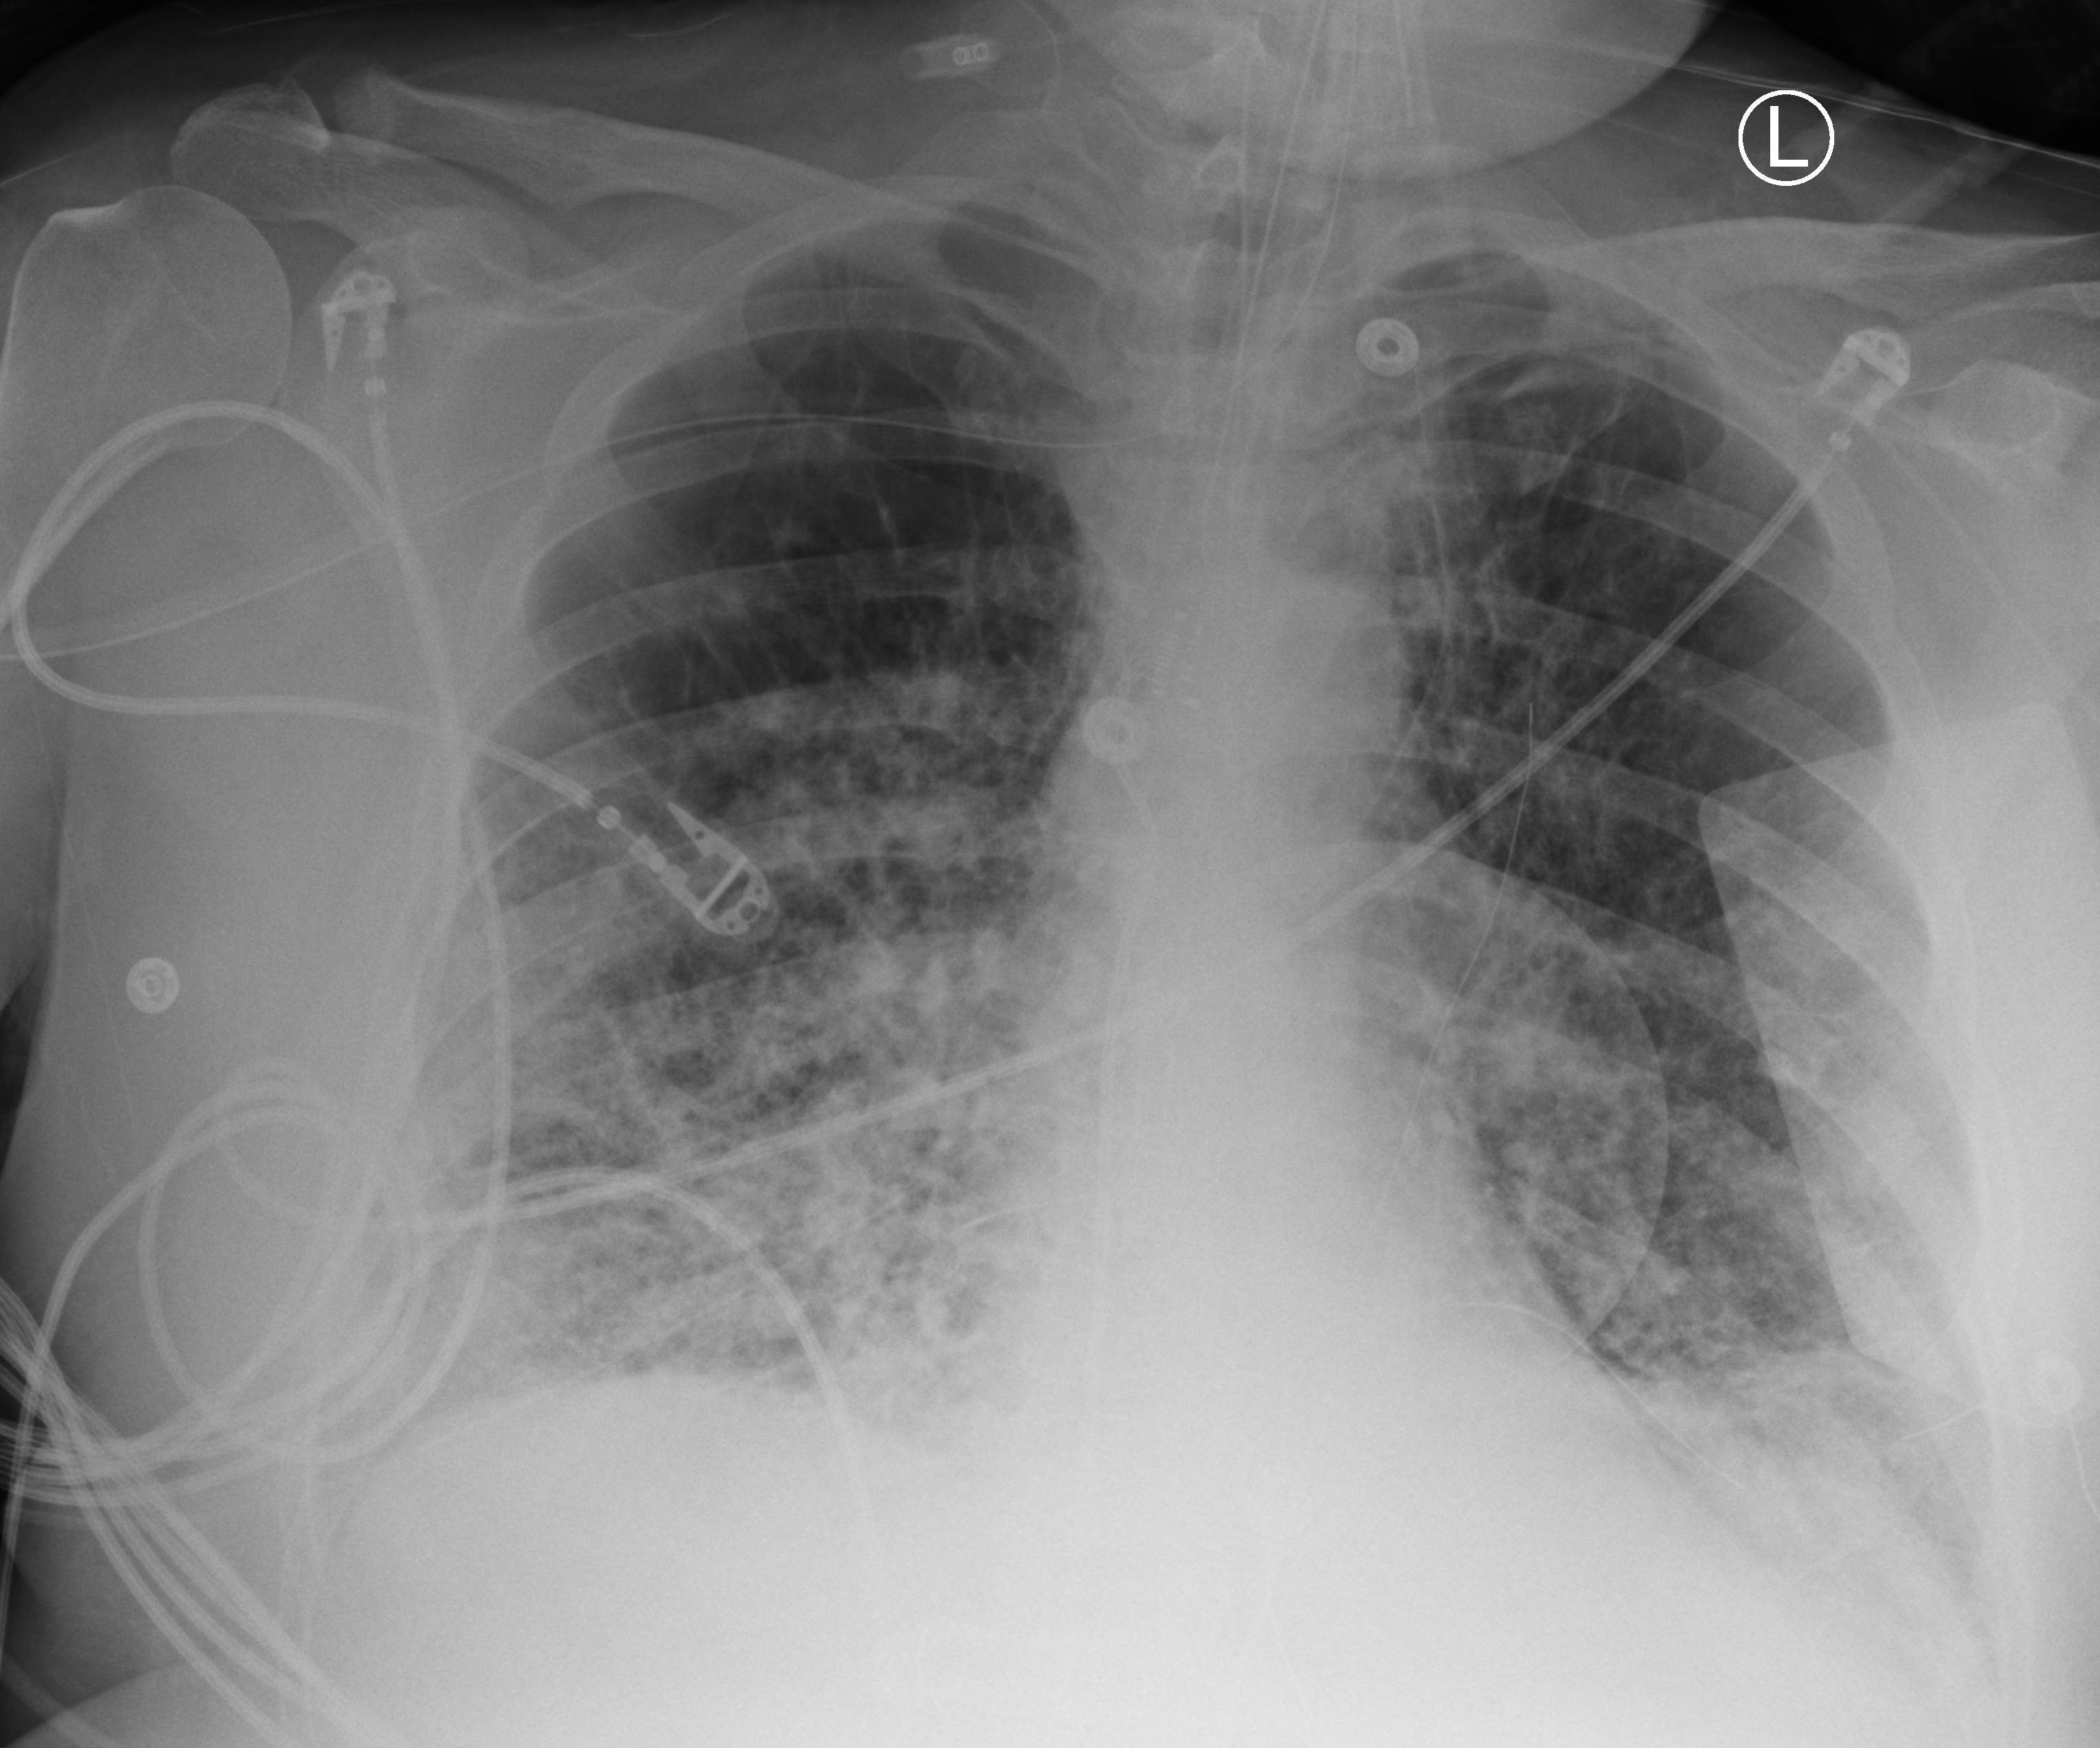
Bedside chest radiograph (computed radiography); anteroposterior (AP) projection. Patient hospitalised with COVID-19, aged 18–59 years.
Hospital-stay facts (about this admission, not read from this image; timing relative to this image not recorded):
- admitted to intensive care during this hospital stay: yes
- mechanically ventilated during this hospital stay: yes
- other chronic lung disease (admission record): yes